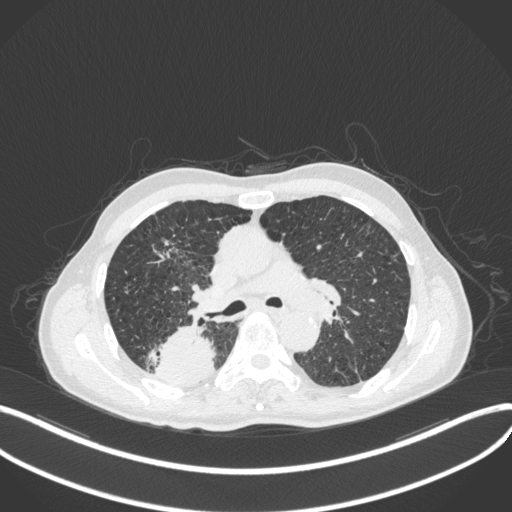
Chest CT, one axial slice; position 286 of 423 along the scan axis; lung window (W 1500 / L -600 HU); 1 mm slice thickness; 512 × 512 image matrix. Patient: male, 79 years. Case-level facts recorded for this patient, not image findings: clinical TNM (as recorded): T3 N0 M0.
Outlined on this slice (rectangle marked by the reading radiologist):
- lung tumour (recorded histology: adenocarcinoma): bounding box <155,320,218,389> (left, top, right, bottom; pixels)